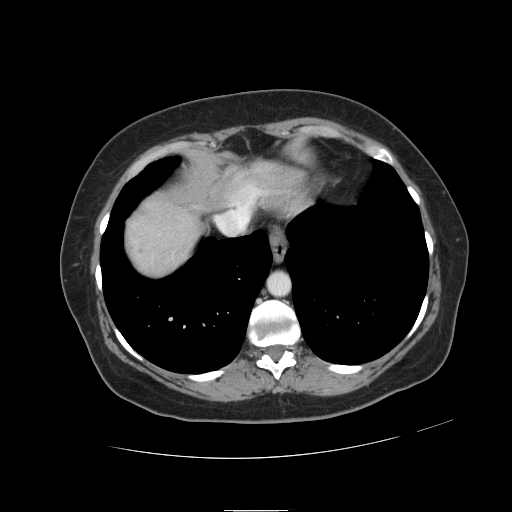
Contrast-enhanced abdominal CT, one axial slice; slice 108 of 121 in the series (ordered by position); 120 kVp; intravenous contrast given; soft-tissue window (W 400 / L 40 HU); 512 × 512 image matrix, field of view 400 × 400 mm. Female patient, age 52 years. From the clinical record (not read from this slice): diagnosis: colorectal cancer liver metastases, imaged before liver resection; multiple liver metastases: yes; largest metastasis: 6.3 cm; disease in both lobes: no.
Annotated regions visible in this slice (expert manual segmentation):
- liver: bounding box [x1, y1, x2, y2] px = [125, 188, 218, 277]